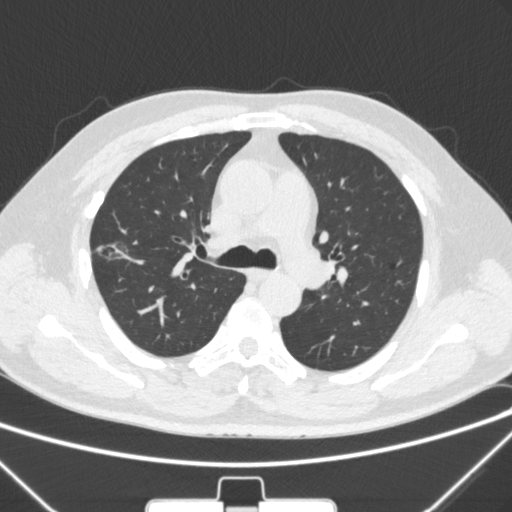
Chest CT, one axial slice; position 201 of 320 along the scan axis; 120 kVp; lung window (W 1500 / L -600 HU); 1 mm slice thickness; 512 × 512 image matrix, field of view 350 × 350 mm. Male patient, age 58 years. From the clinical record (not read from this slice): clinical TNM (as recorded): T1c N0 M0; histopathological grade: G2.
Structures marked on this image (bounding box drawn by a radiologist):
- lung tumour (recorded histology: adenocarcinoma): bounding box [x1, y1, x2, y2] px = [92, 230, 133, 270]